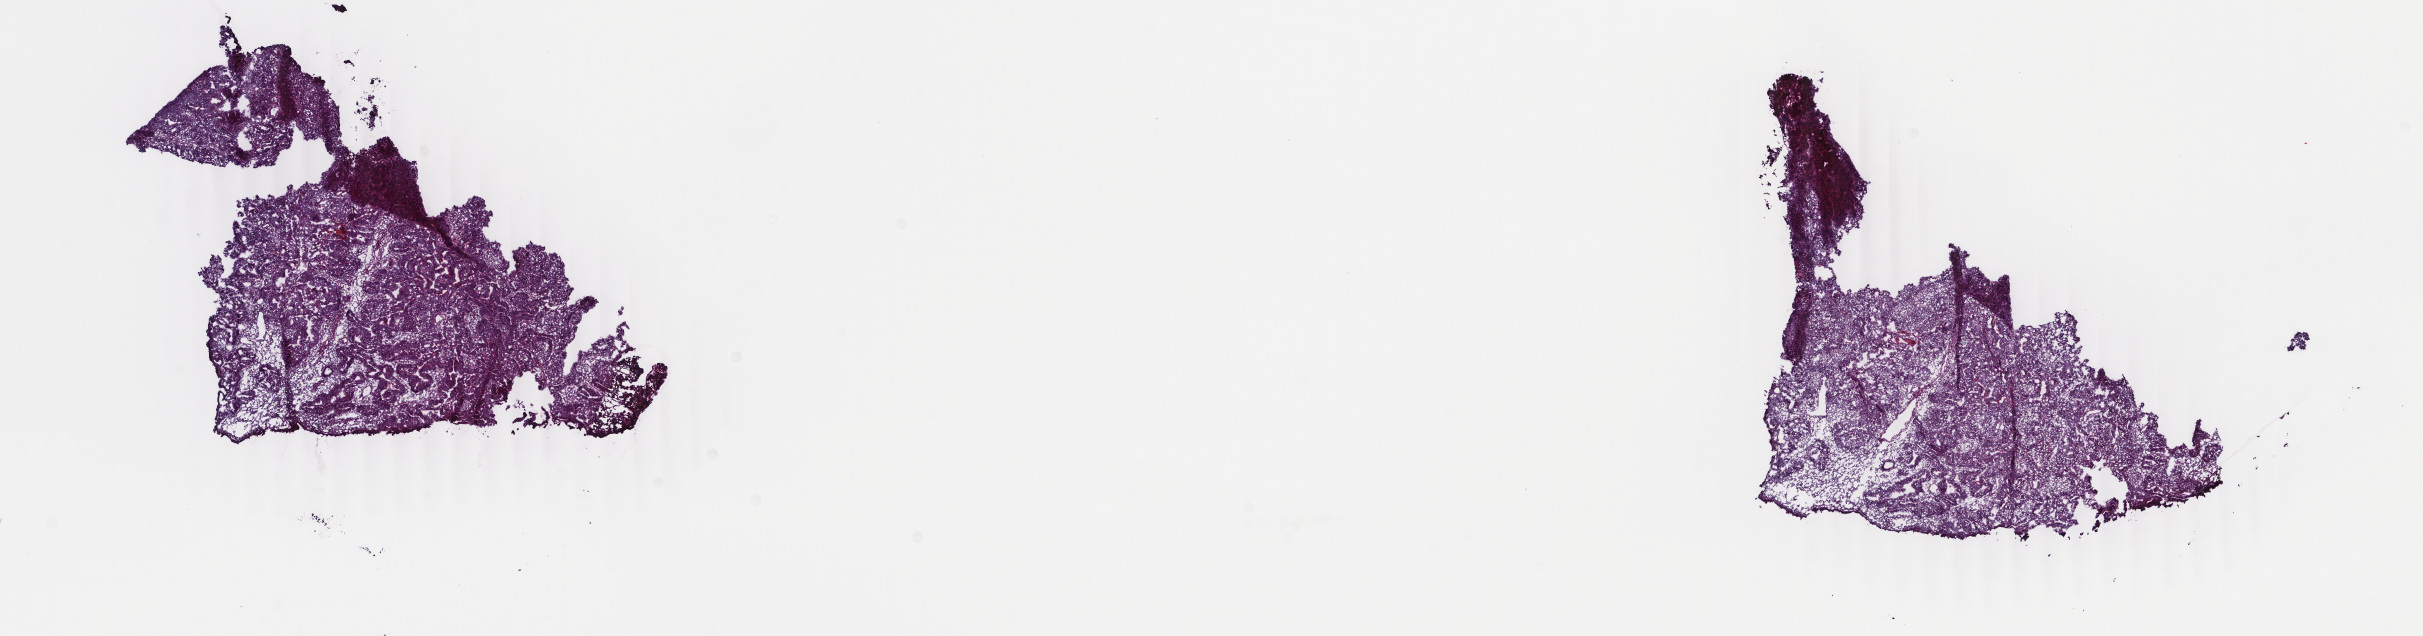
Whole-slide histology image, H&E-stained — whole scanned area (about 19.3 x 5.1 mm) shown as a low-resolution overview. Frozen section from the top of the tissue portion. Sample: primary tumour, uterus. Female, age 48 years at initial diagnosis.
Histologic diagnosis: Endometrioid adenocarcinoma, NOS (endometrium).